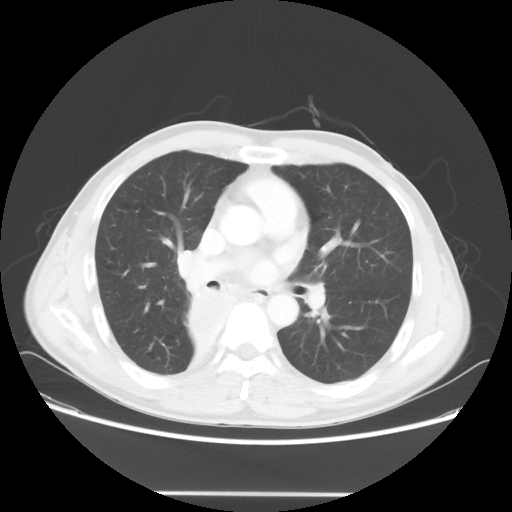
Chest CT, one axial slice; reconstruction kernel STANDARD; lung window (W 1500 / L -600 HU); 5 mm slice thickness; 512 × 512 image matrix, field of view 393 × 393 mm. Patient: male, 47 years. From the clinical record (not read from this slice): clinical TNM (as recorded): T2 N0 M0.
Structures marked on this image (rectangle marked by the reading radiologist):
- lung tumour (recorded histology: squamous cell carcinoma): bounding box [x1, y1, x2, y2] px = [181, 280, 243, 358]